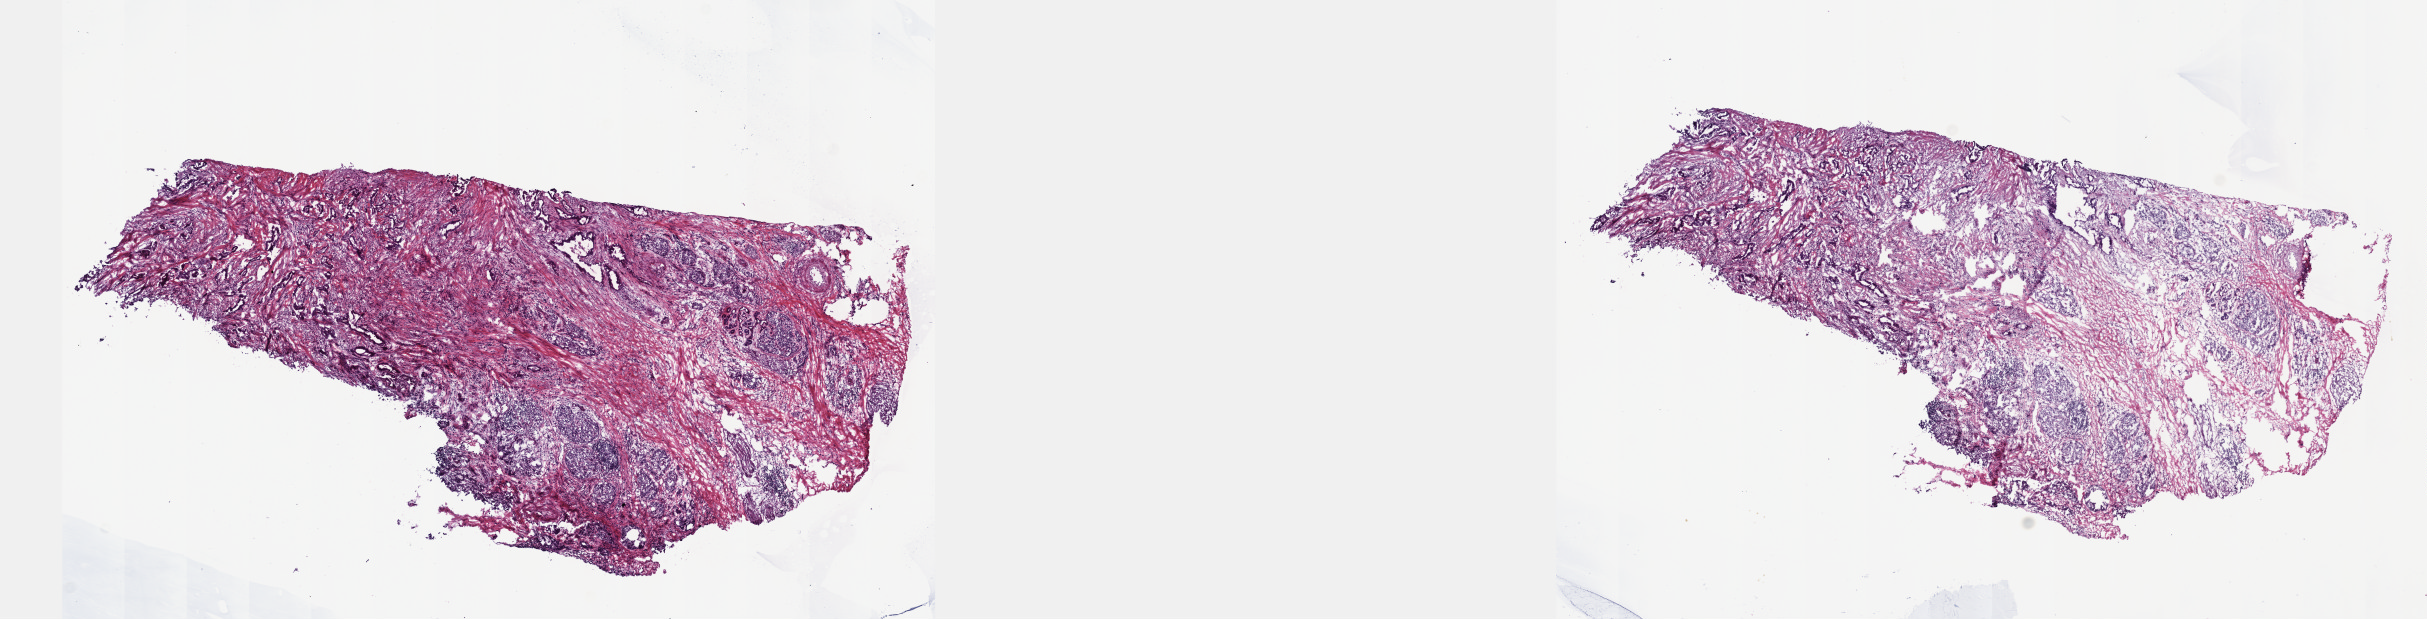
Whole-slide histology image, H&E, a low-resolution overview of the entire scanned area, about 19.6 x 5.0 mm (acquisition: 40x scan). Frozen section from the top of the tissue portion. Sample: primary tumour, pancreas. Male, age 57 years at initial diagnosis. Histologic grade: G1 (well differentiated). Composition of this section per pathologist review: tumour cells 70%, tumour nuclei 70%, normal cells 0%, stromal cells 30%, necrosis 0%. Inflammatory infiltration, as recorded: lymphocyte infiltration 40%, monocyte infiltration 20%, neutrophil infiltration 20%.
Histologic diagnosis: Infiltrating duct carcinoma, NOS (head of pancreas). Lymph nodes positive (case pathology): 0 of 13 examined.